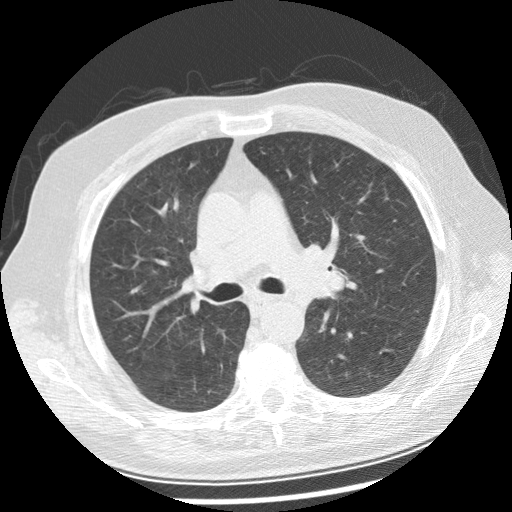
Low-dose screening chest CT, one axial slice. Reconstruction kernel STANDARD. 120 kVp. Lung window (W 1500 / L -600 HU). 2.5 mm slice thickness. 512 × 512 image matrix.
Outlined on this slice (manually delineated by an expert):
- lesion 1 (tumor, left main bronchus): bounding box [x1, y1, x2, y2] px = [309, 270, 347, 298]